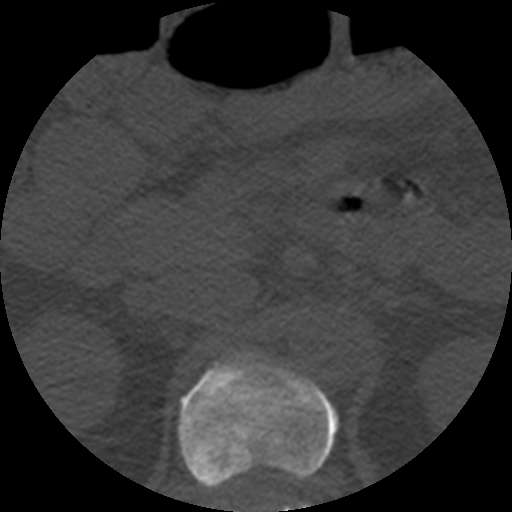
CT including the spine, one axial slice. Position 205 of 508 along the scan axis. 120 kVp. Bone window (W 1800 / L 400 HU). 1.25 mm slice thickness. 512 × 512 image matrix, field of view 160 × 160 mm. Patient age 57 years. Case-level facts recorded for this patient, not image findings: primary cancer: prostate.
Annotated regions visible in this slice (semi-automatically segmented with operator editing):
- L1 vertebra: box from (x=297, y=504) to (x=309, y=512) px
- T12 vertebra: (x=177, y=352)–(x=337, y=512)